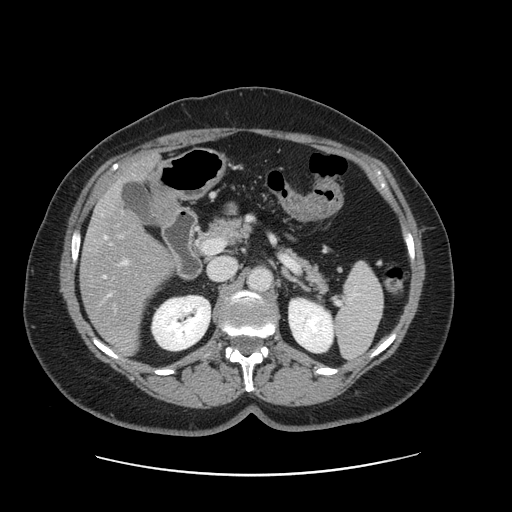
Contrast-enhanced abdominal CT, one axial slice. Slice 74 of 161 in the series (ordered by position). Intravenous contrast given. Soft-tissue window (W 400 / L 40 HU). 512 × 512 image matrix, field of view 398 × 398 mm. Female patient, age 62 years. From the clinical record (not read from this slice): diagnosis: colorectal cancer liver metastases, imaged before liver resection; multiple liver metastases: no; largest metastasis: 2.5 cm.
Structures marked on this image (expert manual segmentation):
- hepatic veins: bounding box <104,236,111,296> (left, top, right, bottom; pixels)
- liver: <82,158,173,354>
- planned liver remnant (the part of the liver to remain after resection): <119,159,155,186>
- portal vein (with intrahepatic branches): <119,236,127,264>